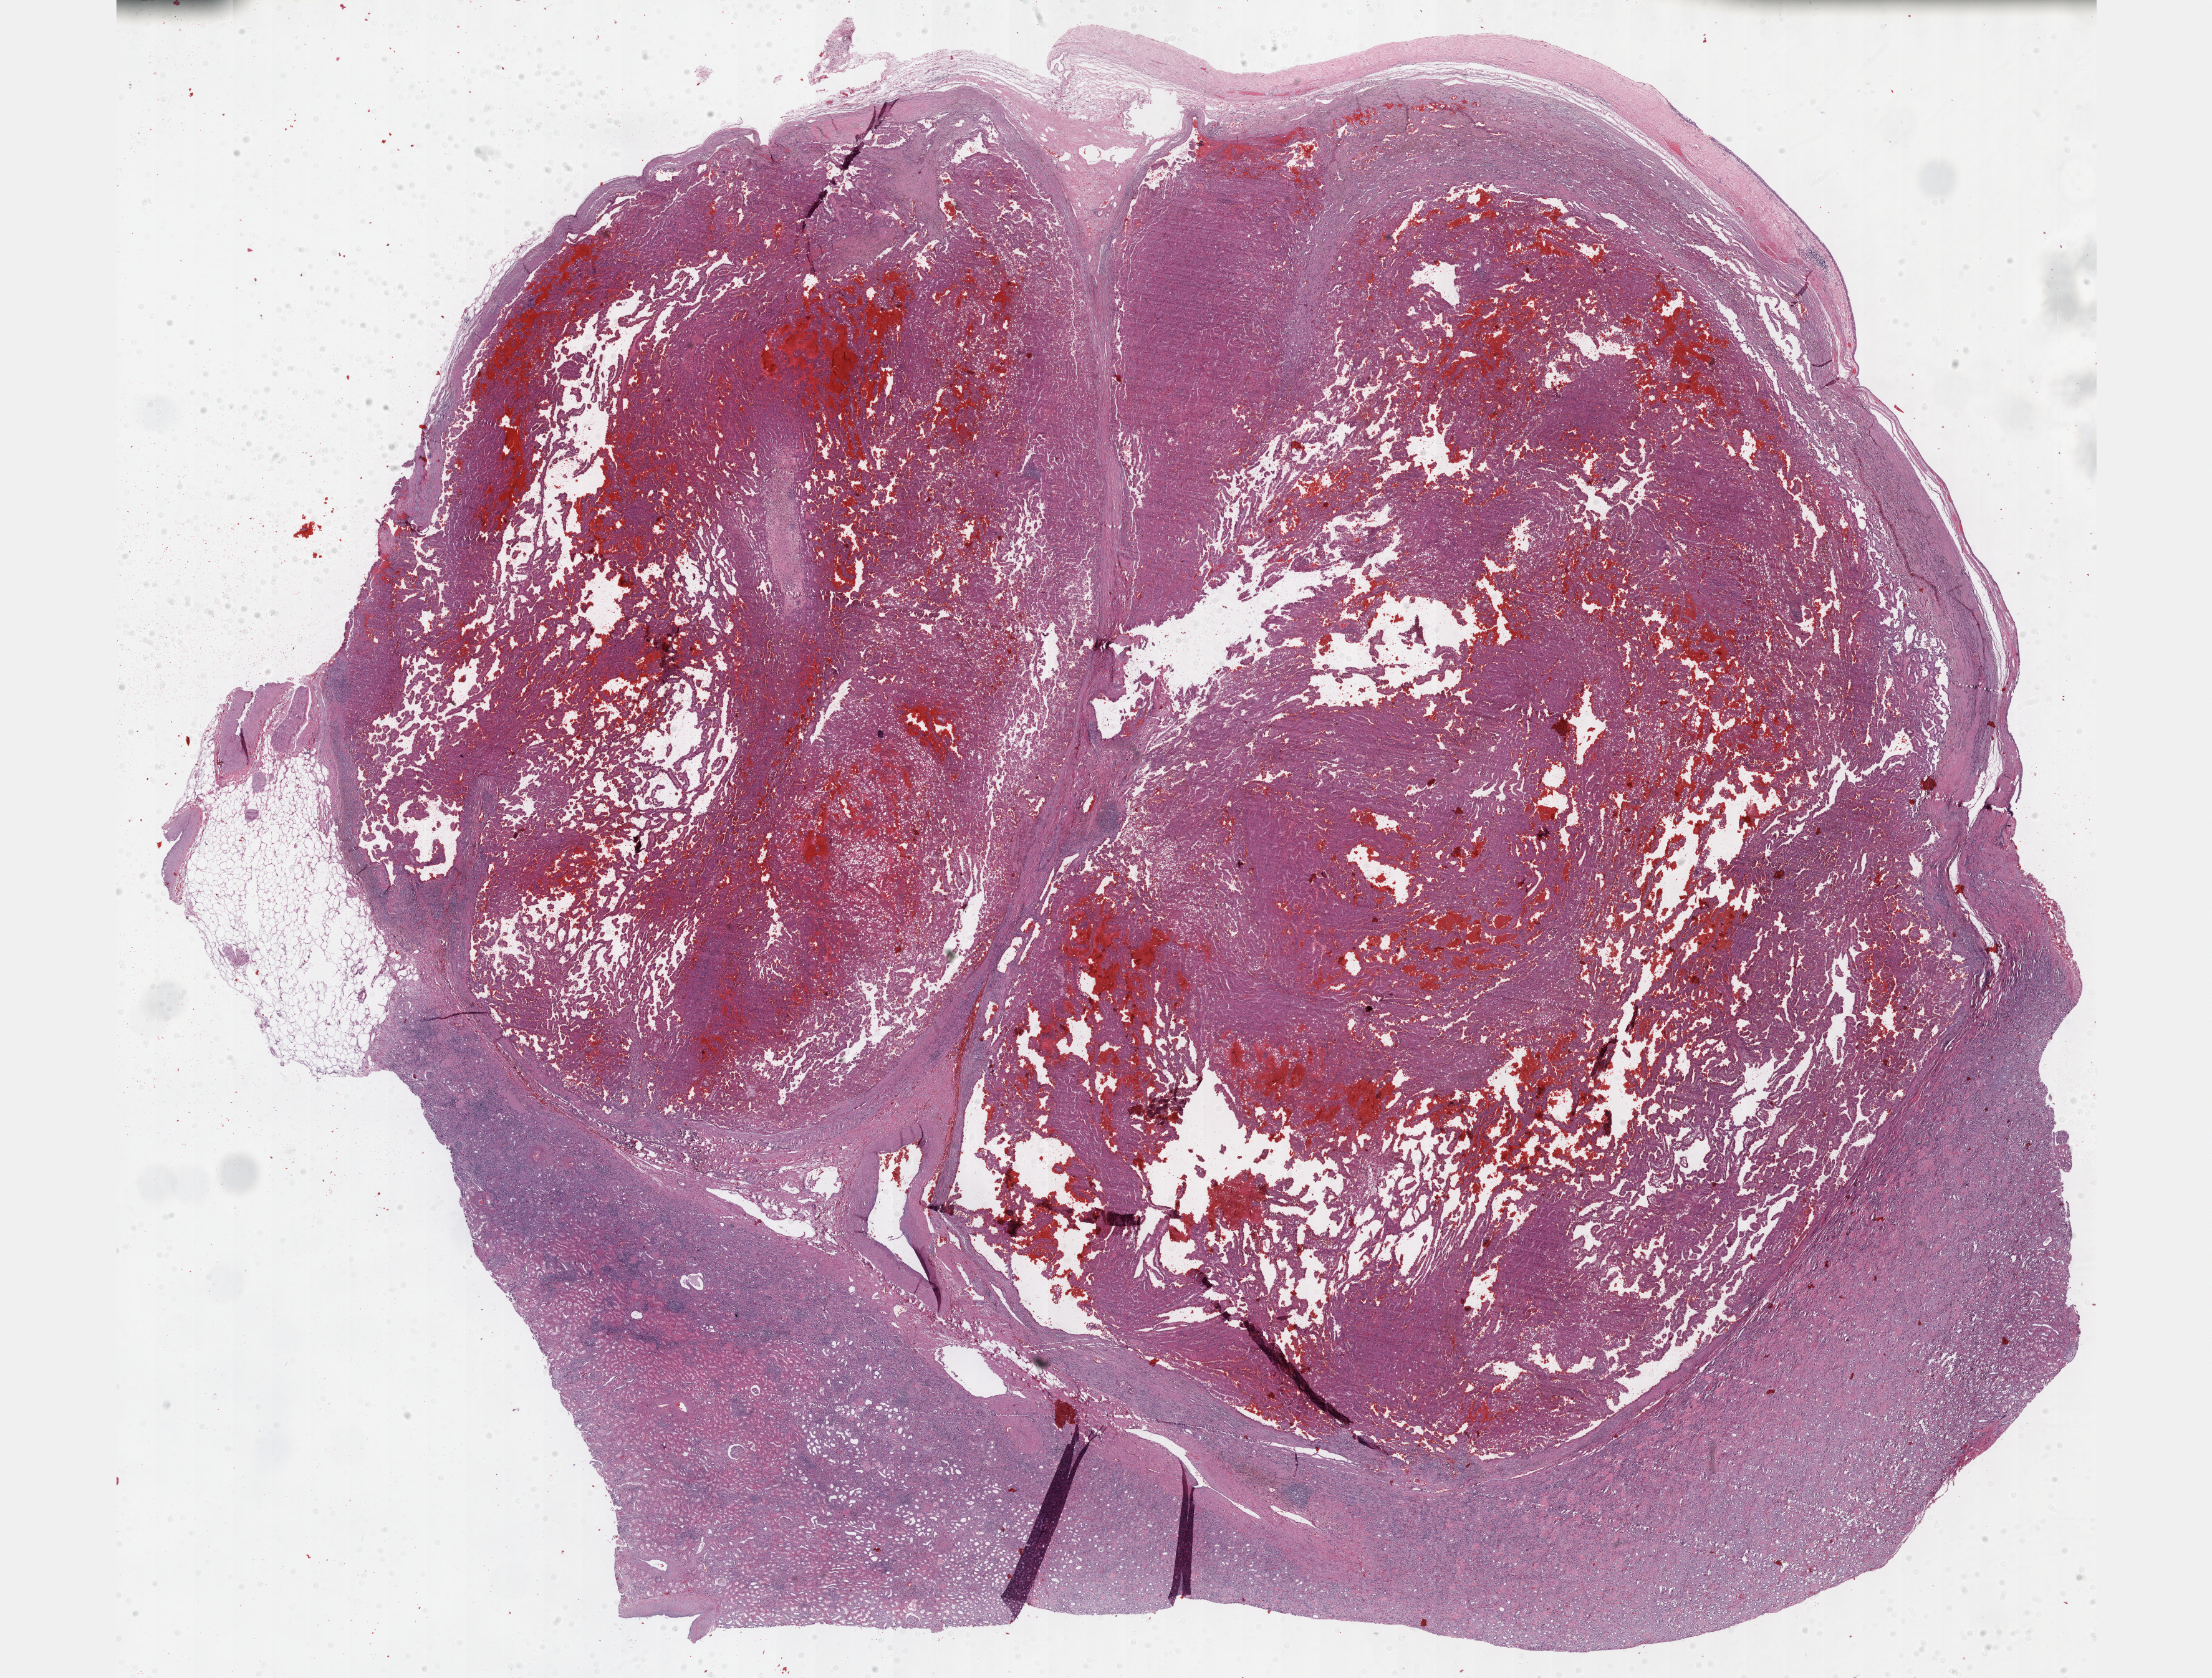
H&E-stained whole-slide image, shown as a low-resolution overview of the whole scanned area (about 28.7 x 21.8 mm), formalin-fixed paraffin-embedded (FFPE) diagnostic section, sample: primary tumour, kidney. Female patient; age at initial diagnosis 81 years.
• histologic diagnosis: Papillary adenocarcinoma, NOS
• AJCC pathologic stage: I